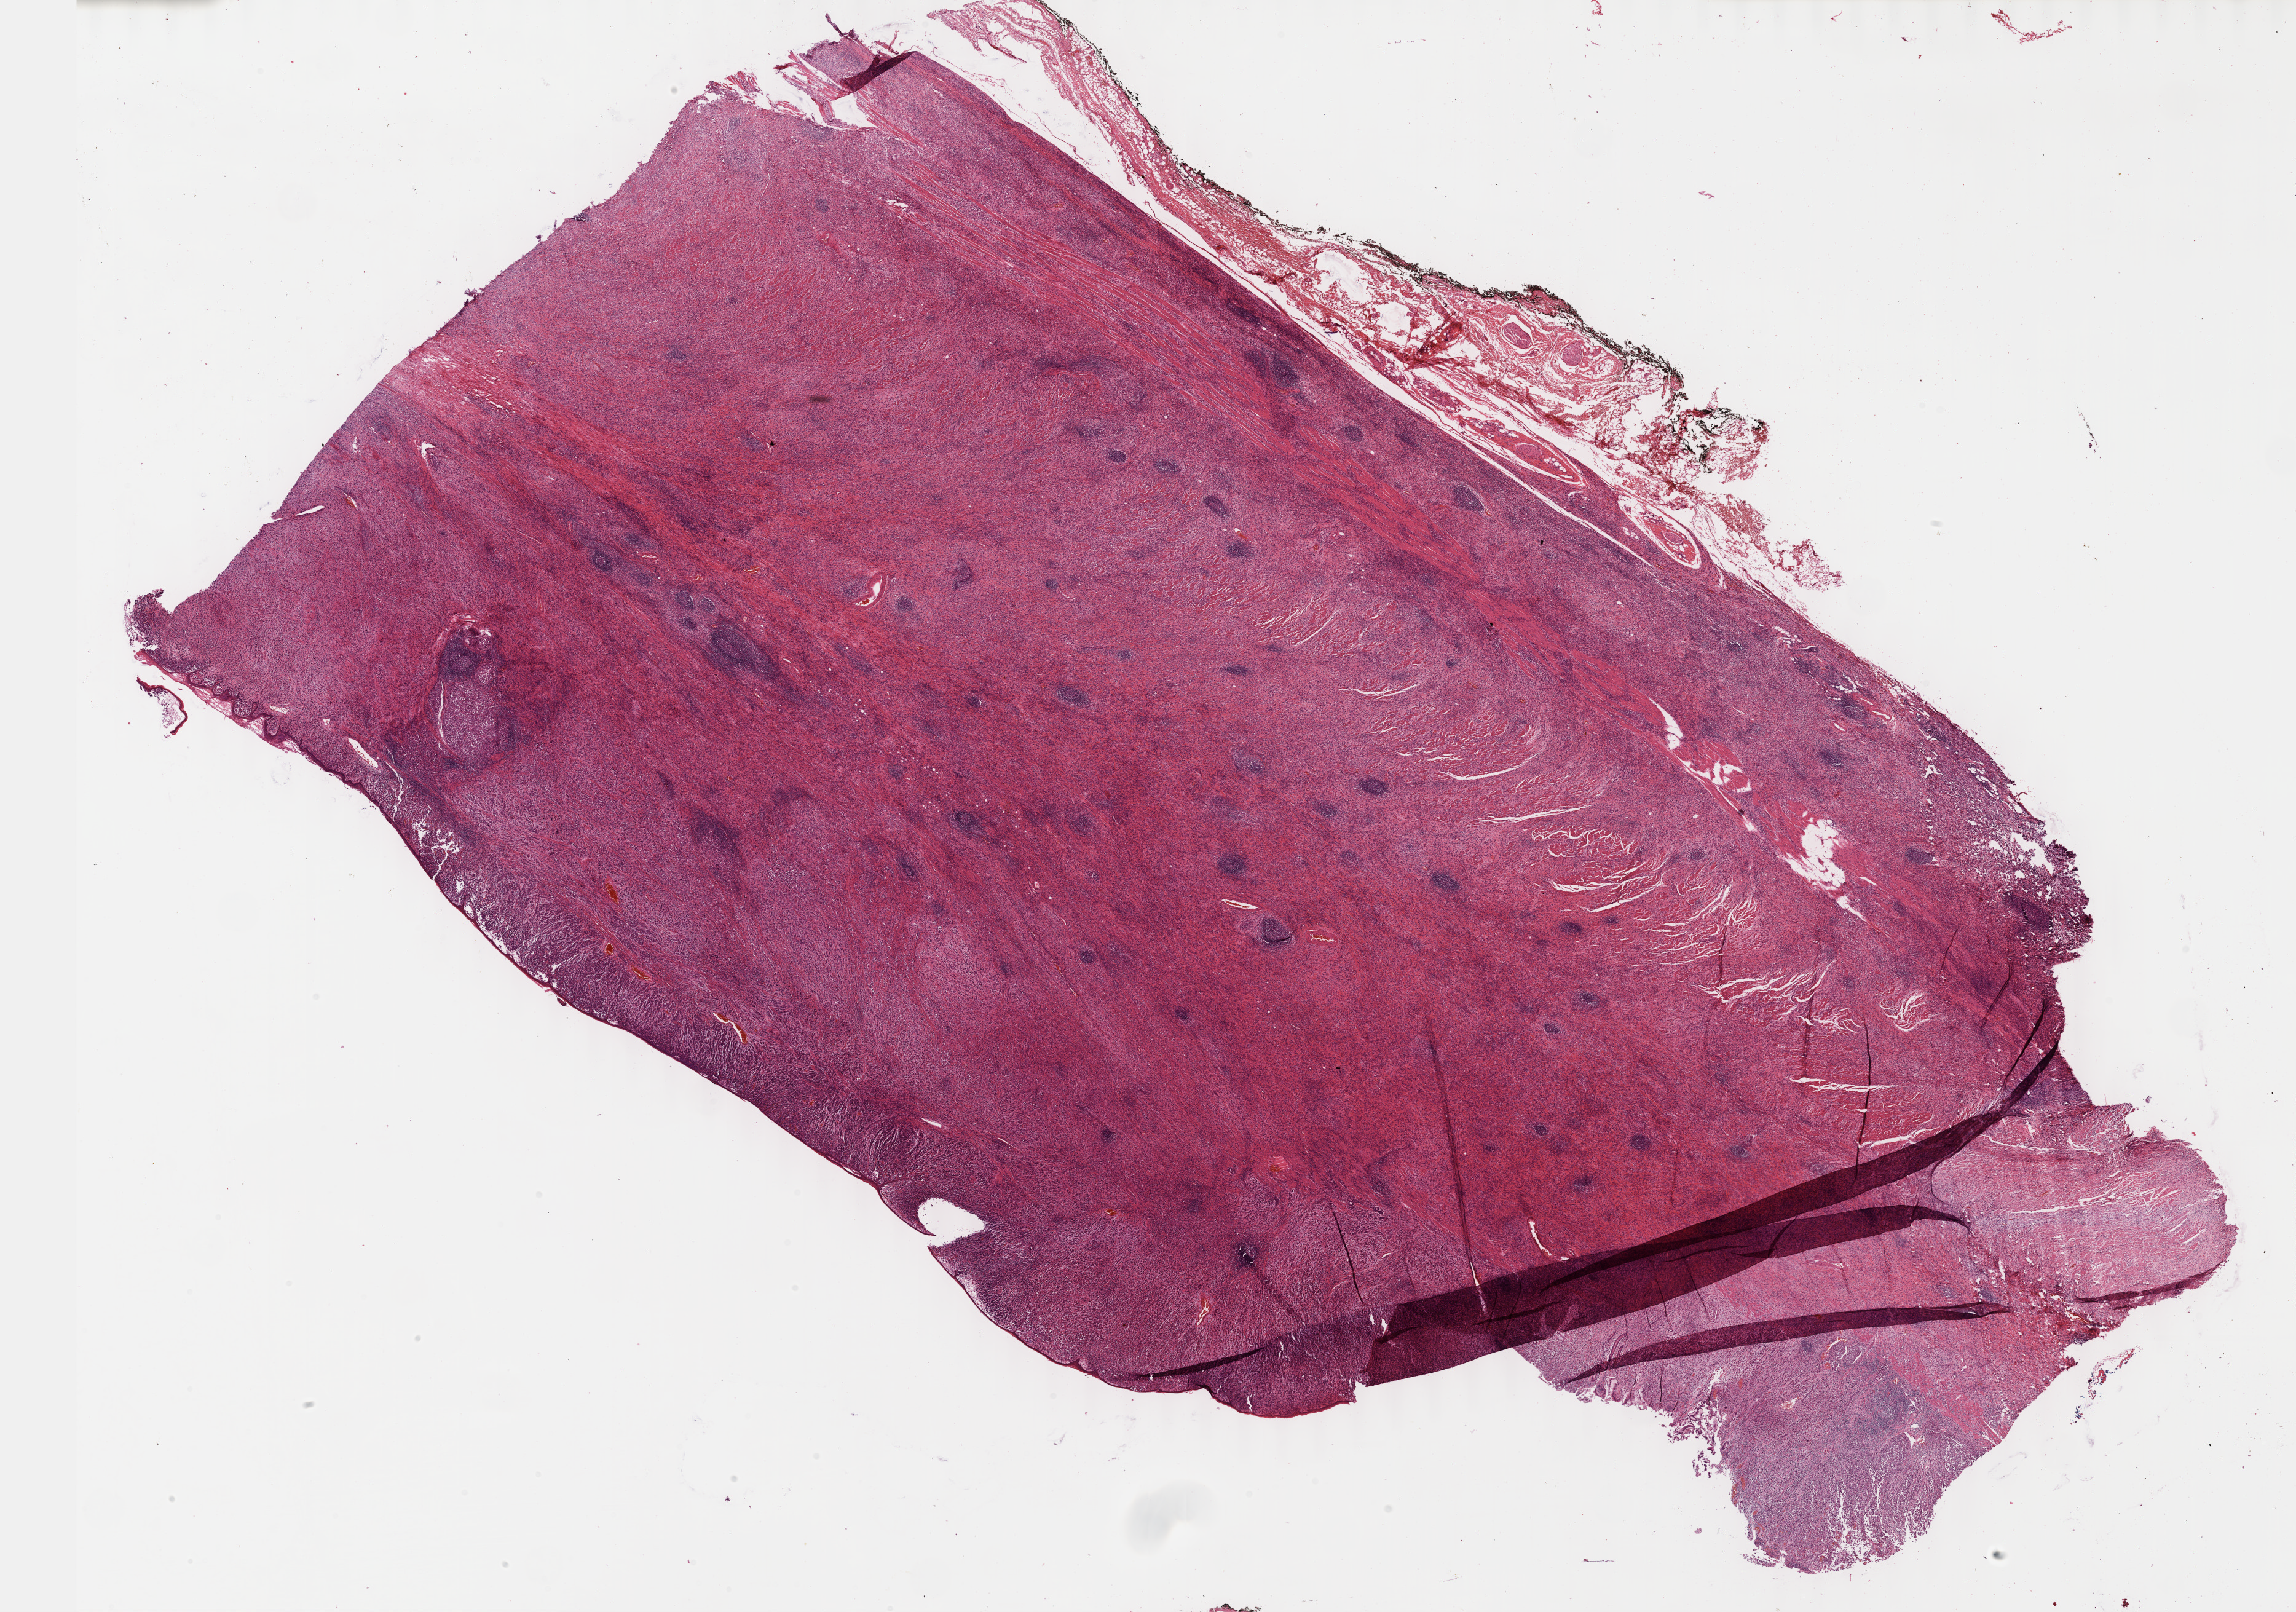
H&E-stained whole-slide image, low-resolution overview of the scanned area, about 30.2 x 21.2 mm. Formalin-fixed paraffin-embedded (FFPE) diagnostic section. Primary tumour sample from the stomach. Patient: male, age at initial diagnosis 56 years. Histologic grade: G3 (poorly differentiated).
Lymph nodes positive (case pathology): 55 of 81 examined. Diagnosis: Signet ring cell carcinoma (cardia, NOS). AJCC pathologic stage: IV (6th edition).